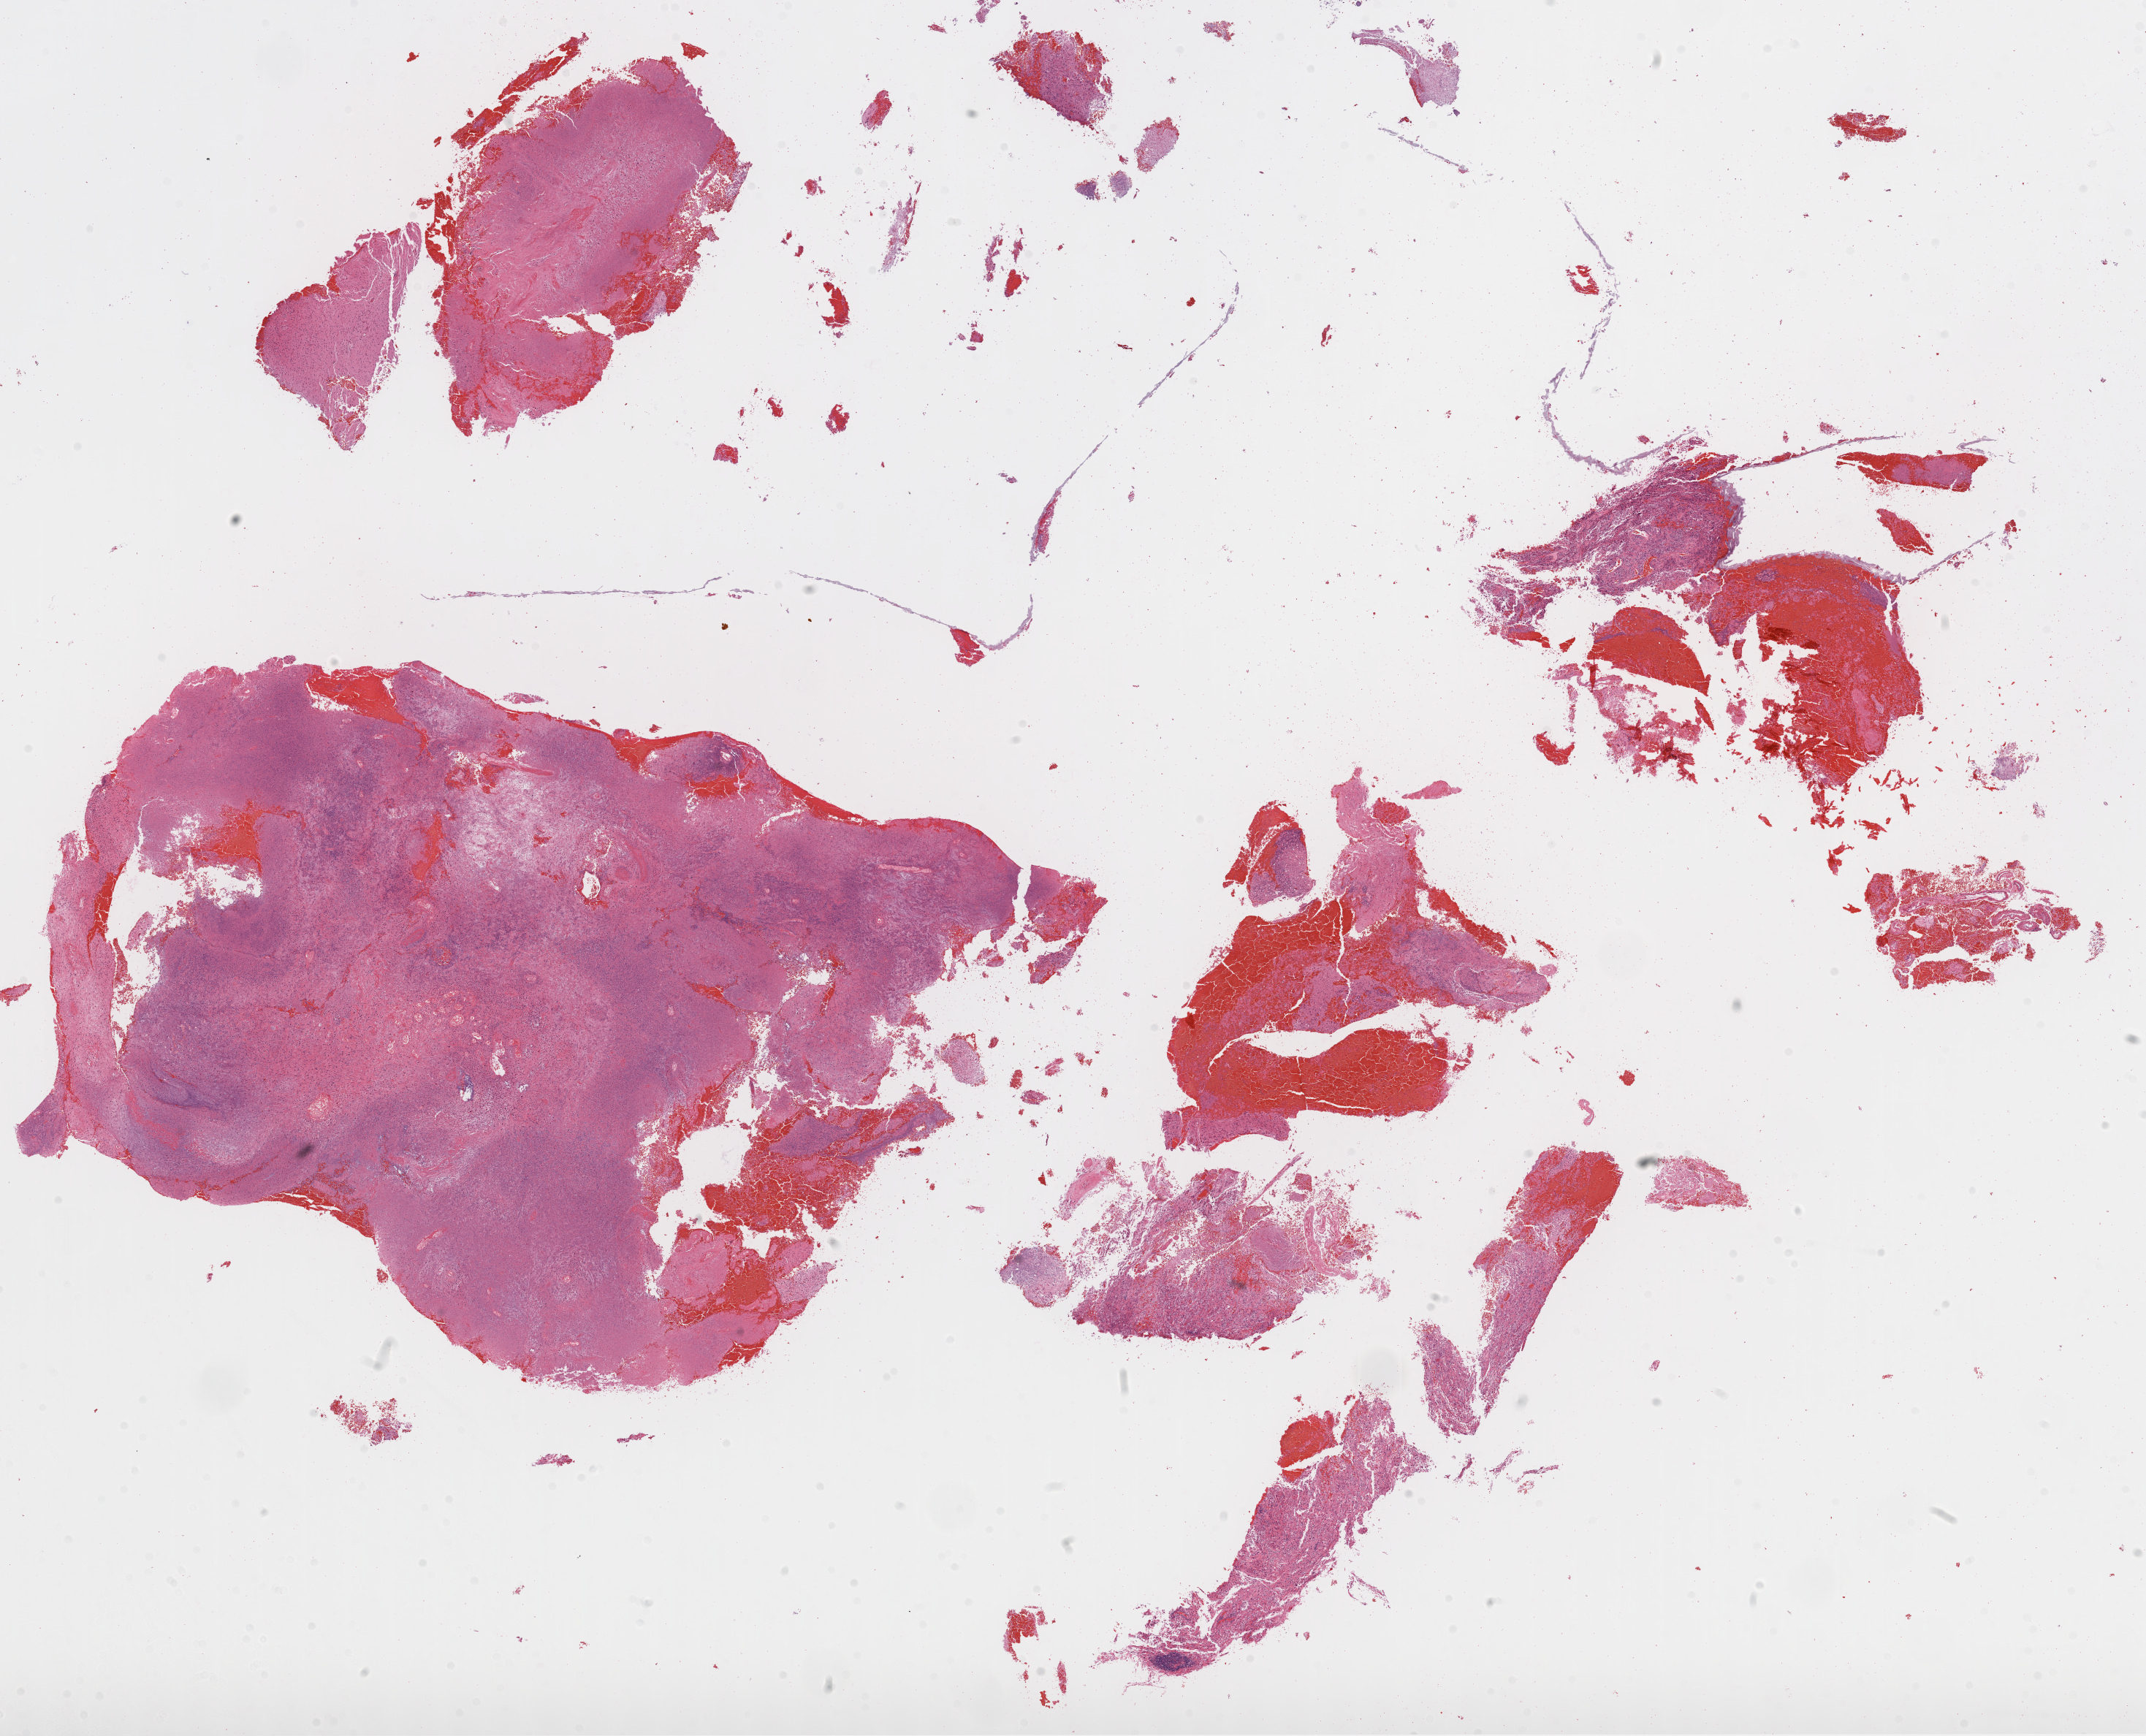
Digitized Hematoxylin and eosin (H&E) stained tissue section (whole slide), low-resolution overview of the scanned area, about 23.7 x 19.2 mm, formalin-fixed paraffin-embedded (FFPE) diagnostic section, sample: primary tumour, brain. Male, age 62 years at initial diagnosis.
Histologic diagnosis: Glioblastoma.